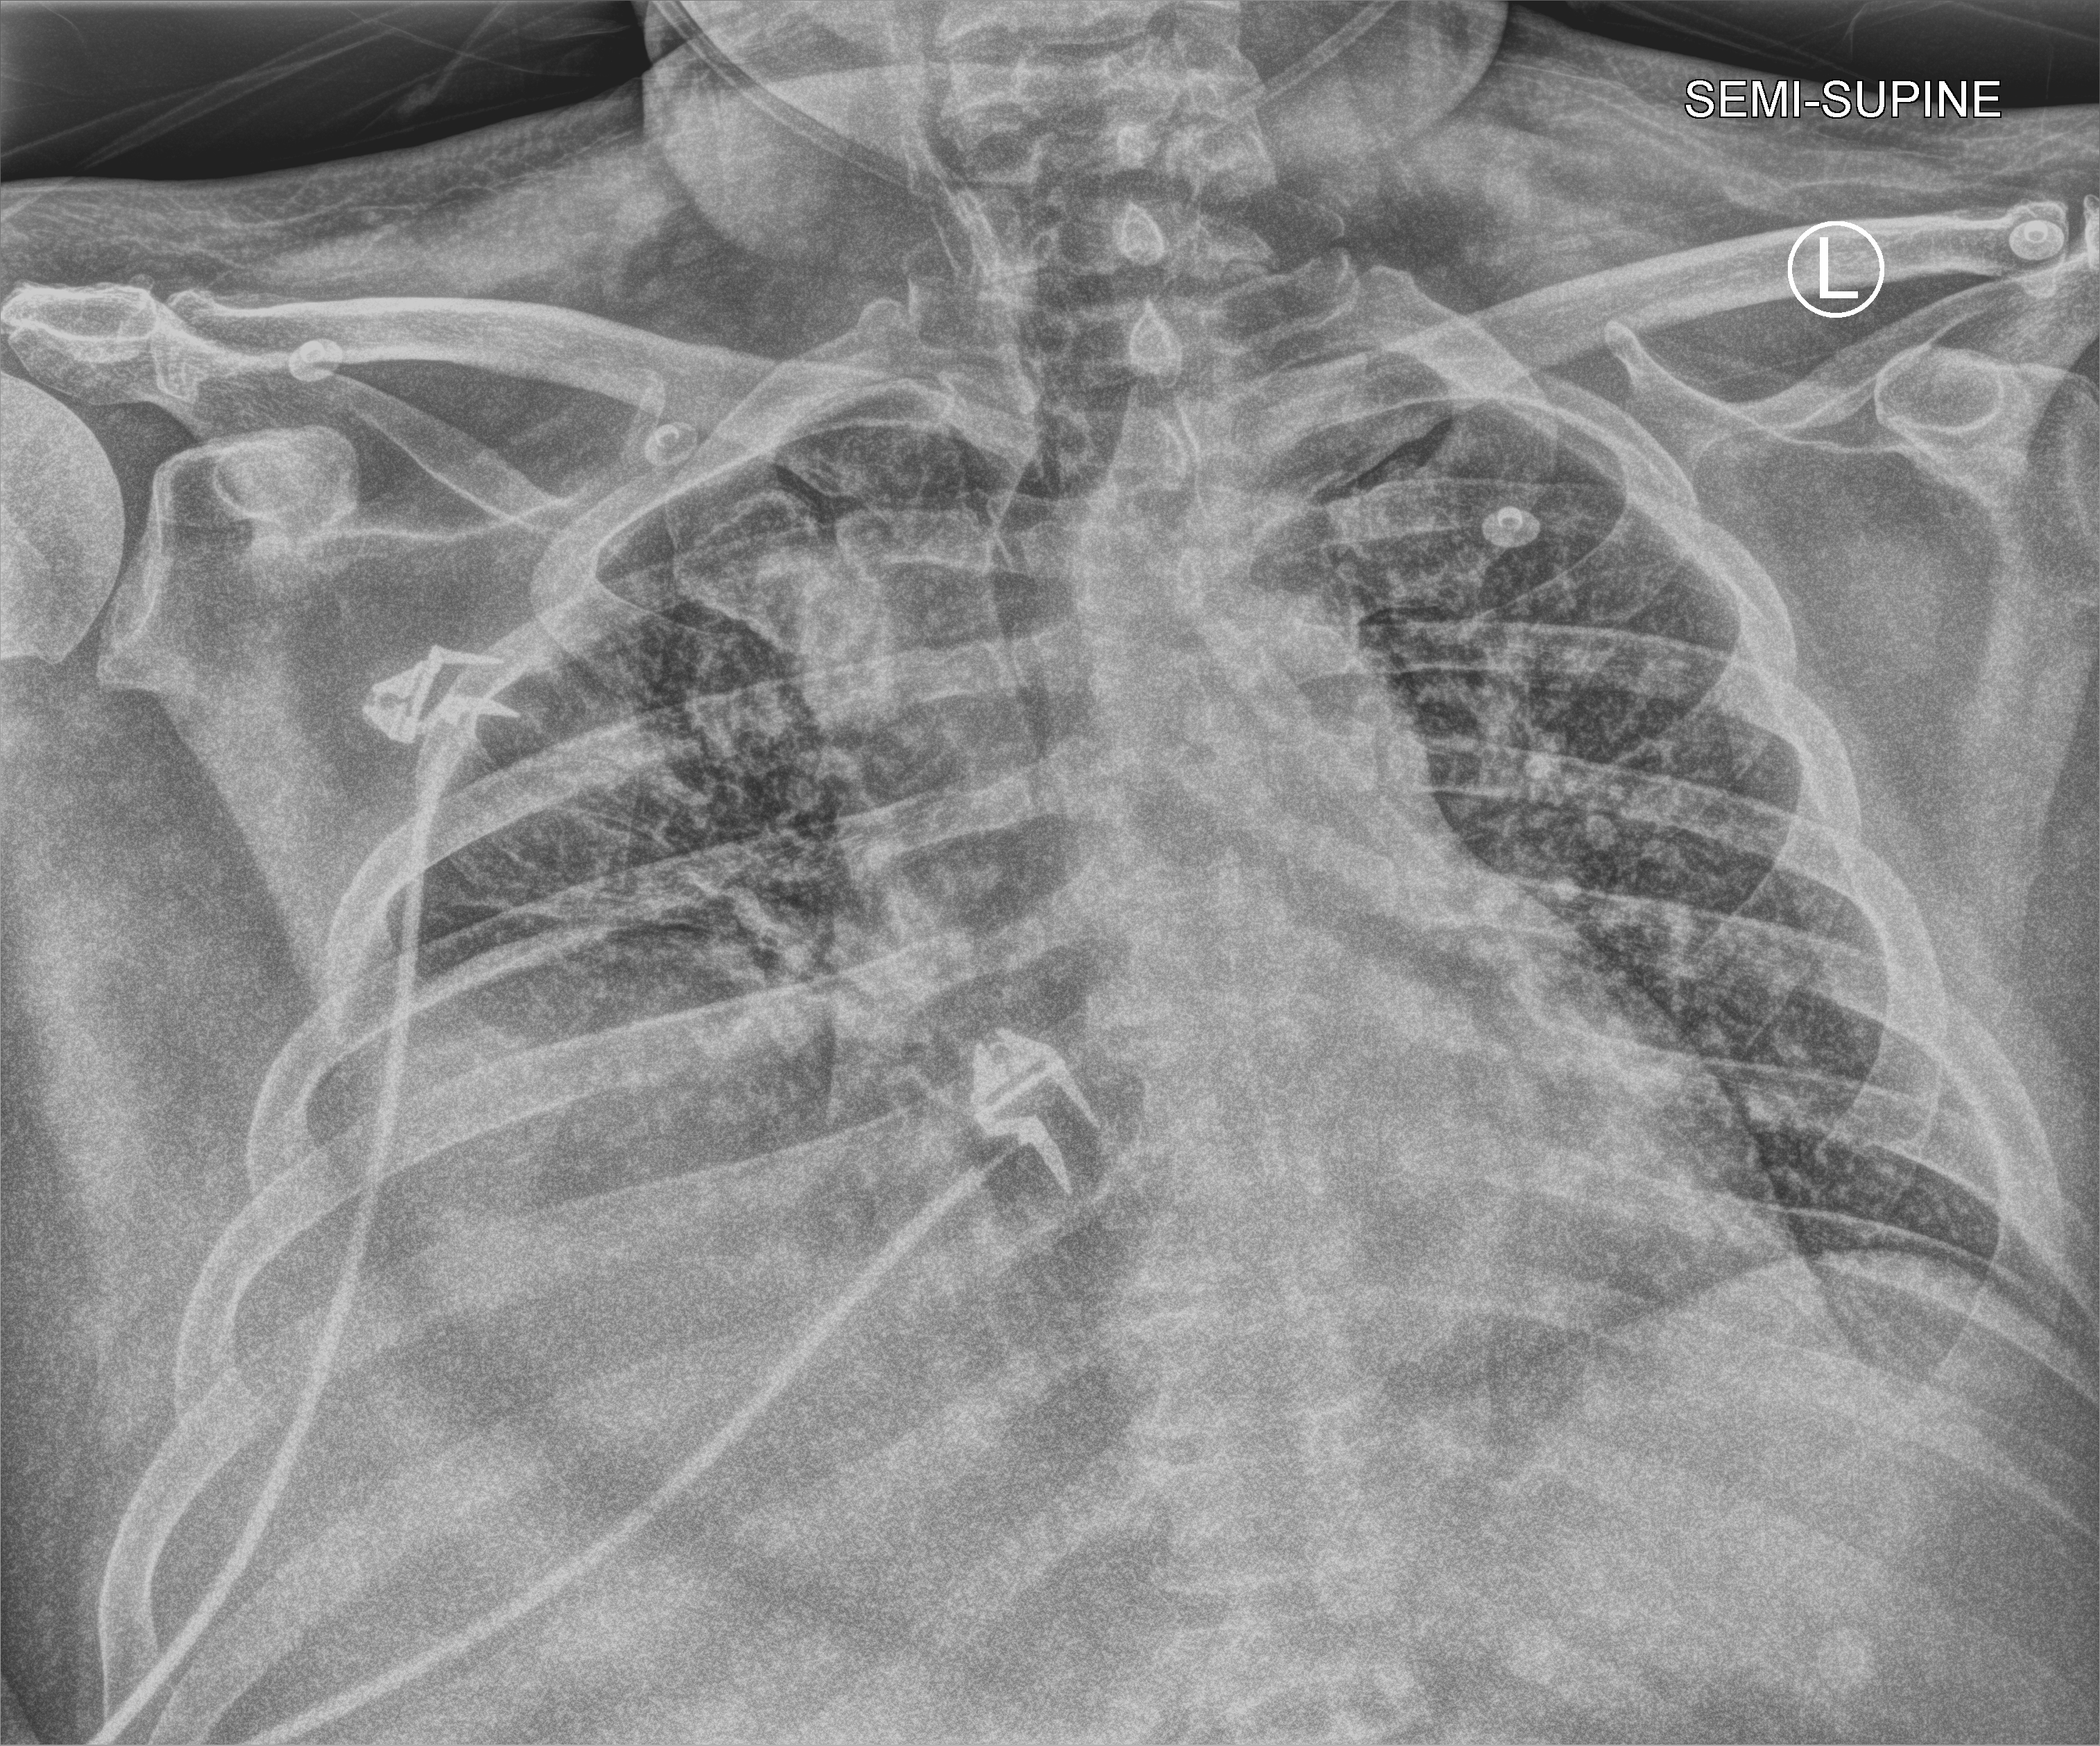
Portable chest radiograph, anteroposterior (AP) projection. Patient hospitalised with COVID-19; male, aged 18–59 years.
Admission-level facts for this patient (not findings on this image; timing relative to this image not recorded):
- COPD (admission record): no
- length of hospital stay: 28 days
- hypertension (admission record): yes